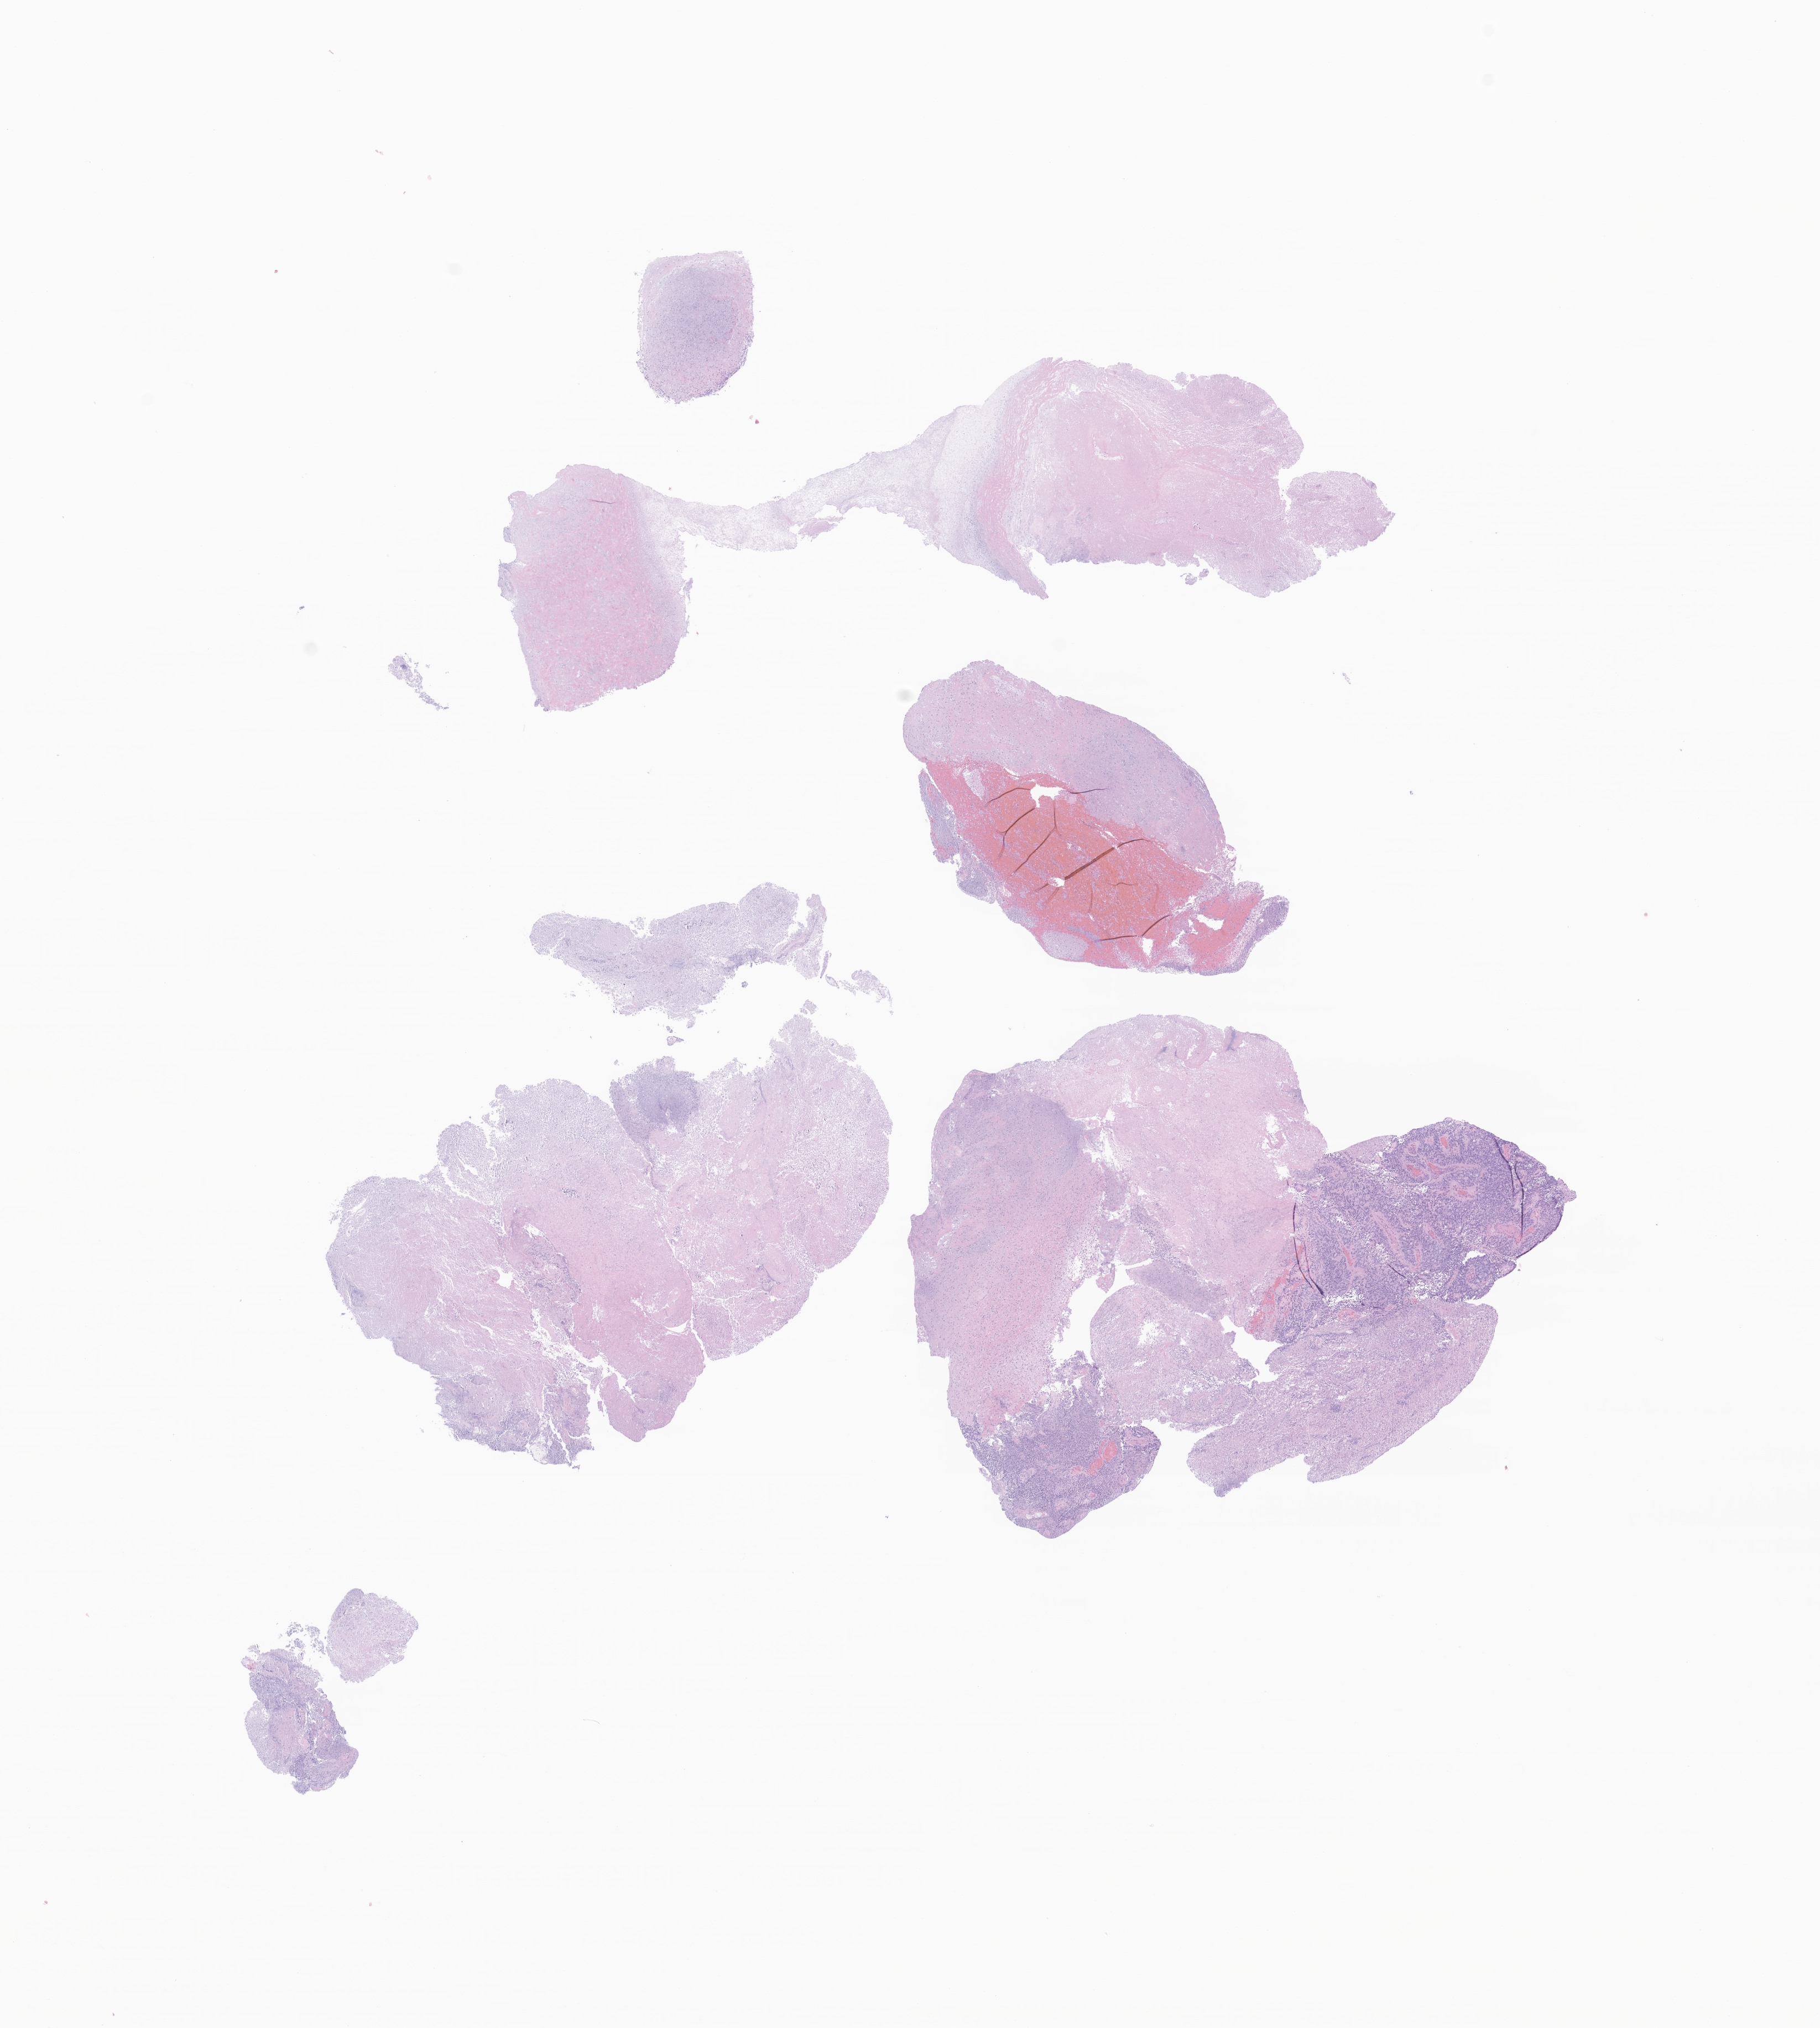
Haematoxylin and eosin whole-slide image of tumor tissue from the brain, a low-resolution overview of the entire scanned area, about 13.9 x 15.5 mm, formalin-fixed paraffin-embedded section. Patient female; age 65 months (5 years 5 months).
Diagnosis (ICD-O-3 morphology term): Neoplasm, malignant.